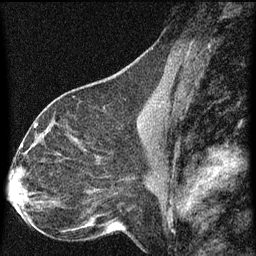
Breast MRI (dynamic contrast-enhanced), one sagittal slice; slice 36 of 60 in the series (ordered by position); dynamic contrast-enhanced series, image 2 of 3 at this slice position (ordered by acquisition); 1.5 T; TE 4.2 ms, TR 8 ms; 256 × 256 image matrix, field of view 180 × 180 mm. Patient: female, 44 years.
Annotated regions visible in this slice (semi-automatic segmentation, software-assisted and operator-edited):
- analysis volume of interest (the breast-tissue region the enhancement analysis was run in; not a lesion): bounding box <49,128,95,169> (left, top, right, bottom; pixels)
- tumour enhancement mask (voxels above the 70 % enhancement threshold inside the analysis volume of interest): <56,138,85,155>